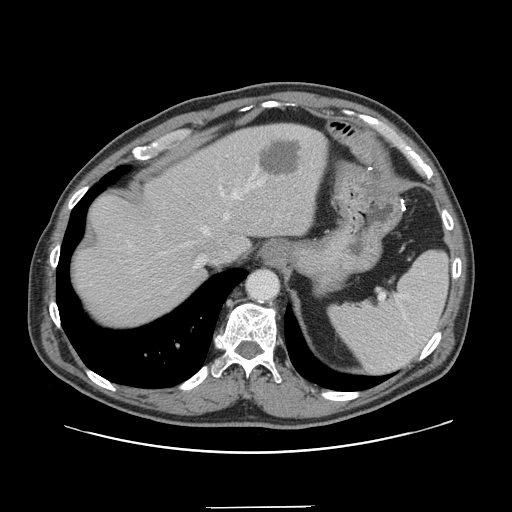
Contrast-enhanced abdominal CT, one axial slice. Slice 118 of 139 in the series (ordered by position). 120 kVp. Intravenous contrast given. Soft-tissue window (W 400 / L 40 HU). 2.5 mm slice thickness. 512 × 512 image matrix, field of view 397 × 397 mm. Male patient, age 64 years. From the clinical record (not read from this slice): diagnosis: colorectal cancer liver metastases, imaged before liver resection.
Annotated regions visible in this slice (manually delineated by an expert):
- hepatic veins: bounding box (x1, y1, x2, y2) in pixels: (192, 181, 262, 268)
- liver: (72, 125, 327, 329)
- planned liver remnant (the part of the liver to remain after resection): (72, 129, 265, 328)
- liver metastasis: (261, 142, 302, 175)